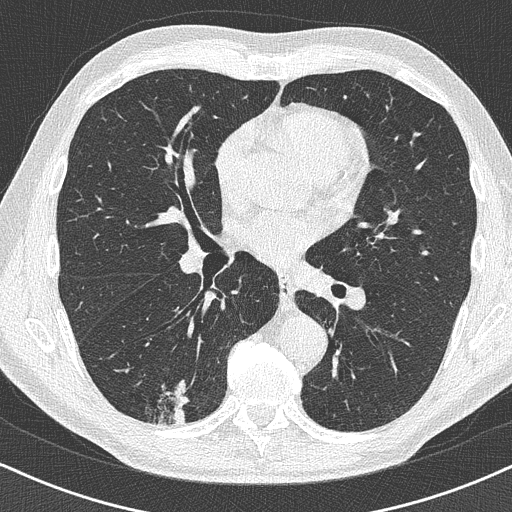
Low-dose screening chest CT, one axial slice. Slice 225 of 438 in the series (ordered by position). Reconstruction kernel B50f. Lung window (W 1500 / L -600 HU). 1 mm slice thickness. 512 × 512 image matrix.
Annotated regions visible in this slice (outlined manually by an expert reader):
- lesion 1 (tumor, lower lobe of right lung): box from (x=175, y=407) to (x=187, y=423) px